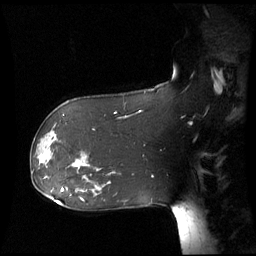
Breast MRI (dynamic contrast-enhanced), one sagittal slice. Slice 40 of 60 in the series (ordered by position). Dynamic contrast-enhanced series, image 2 of 3 at this slice position (ordered by acquisition). 1.5 T. TE 4.2 ms, TR 8.9 ms. 2.7 mm slice thickness. 256 × 256 image matrix. Female patient, age 61 years. Case-level facts recorded for this patient, not image findings: setting: breast cancer imaged before/during neoadjuvant chemotherapy; receptor status: HR-positive, HER2-negative.
Structures marked on this image (semi-automatically segmented with operator editing):
- analysis volume of interest (the breast-tissue region the enhancement analysis was run in; not a lesion): bounding box <30,142,55,177> (left, top, right, bottom; pixels)
- tumour enhancement mask (voxels above the 70 % enhancement threshold inside the analysis volume of interest): <40,156,47,163>